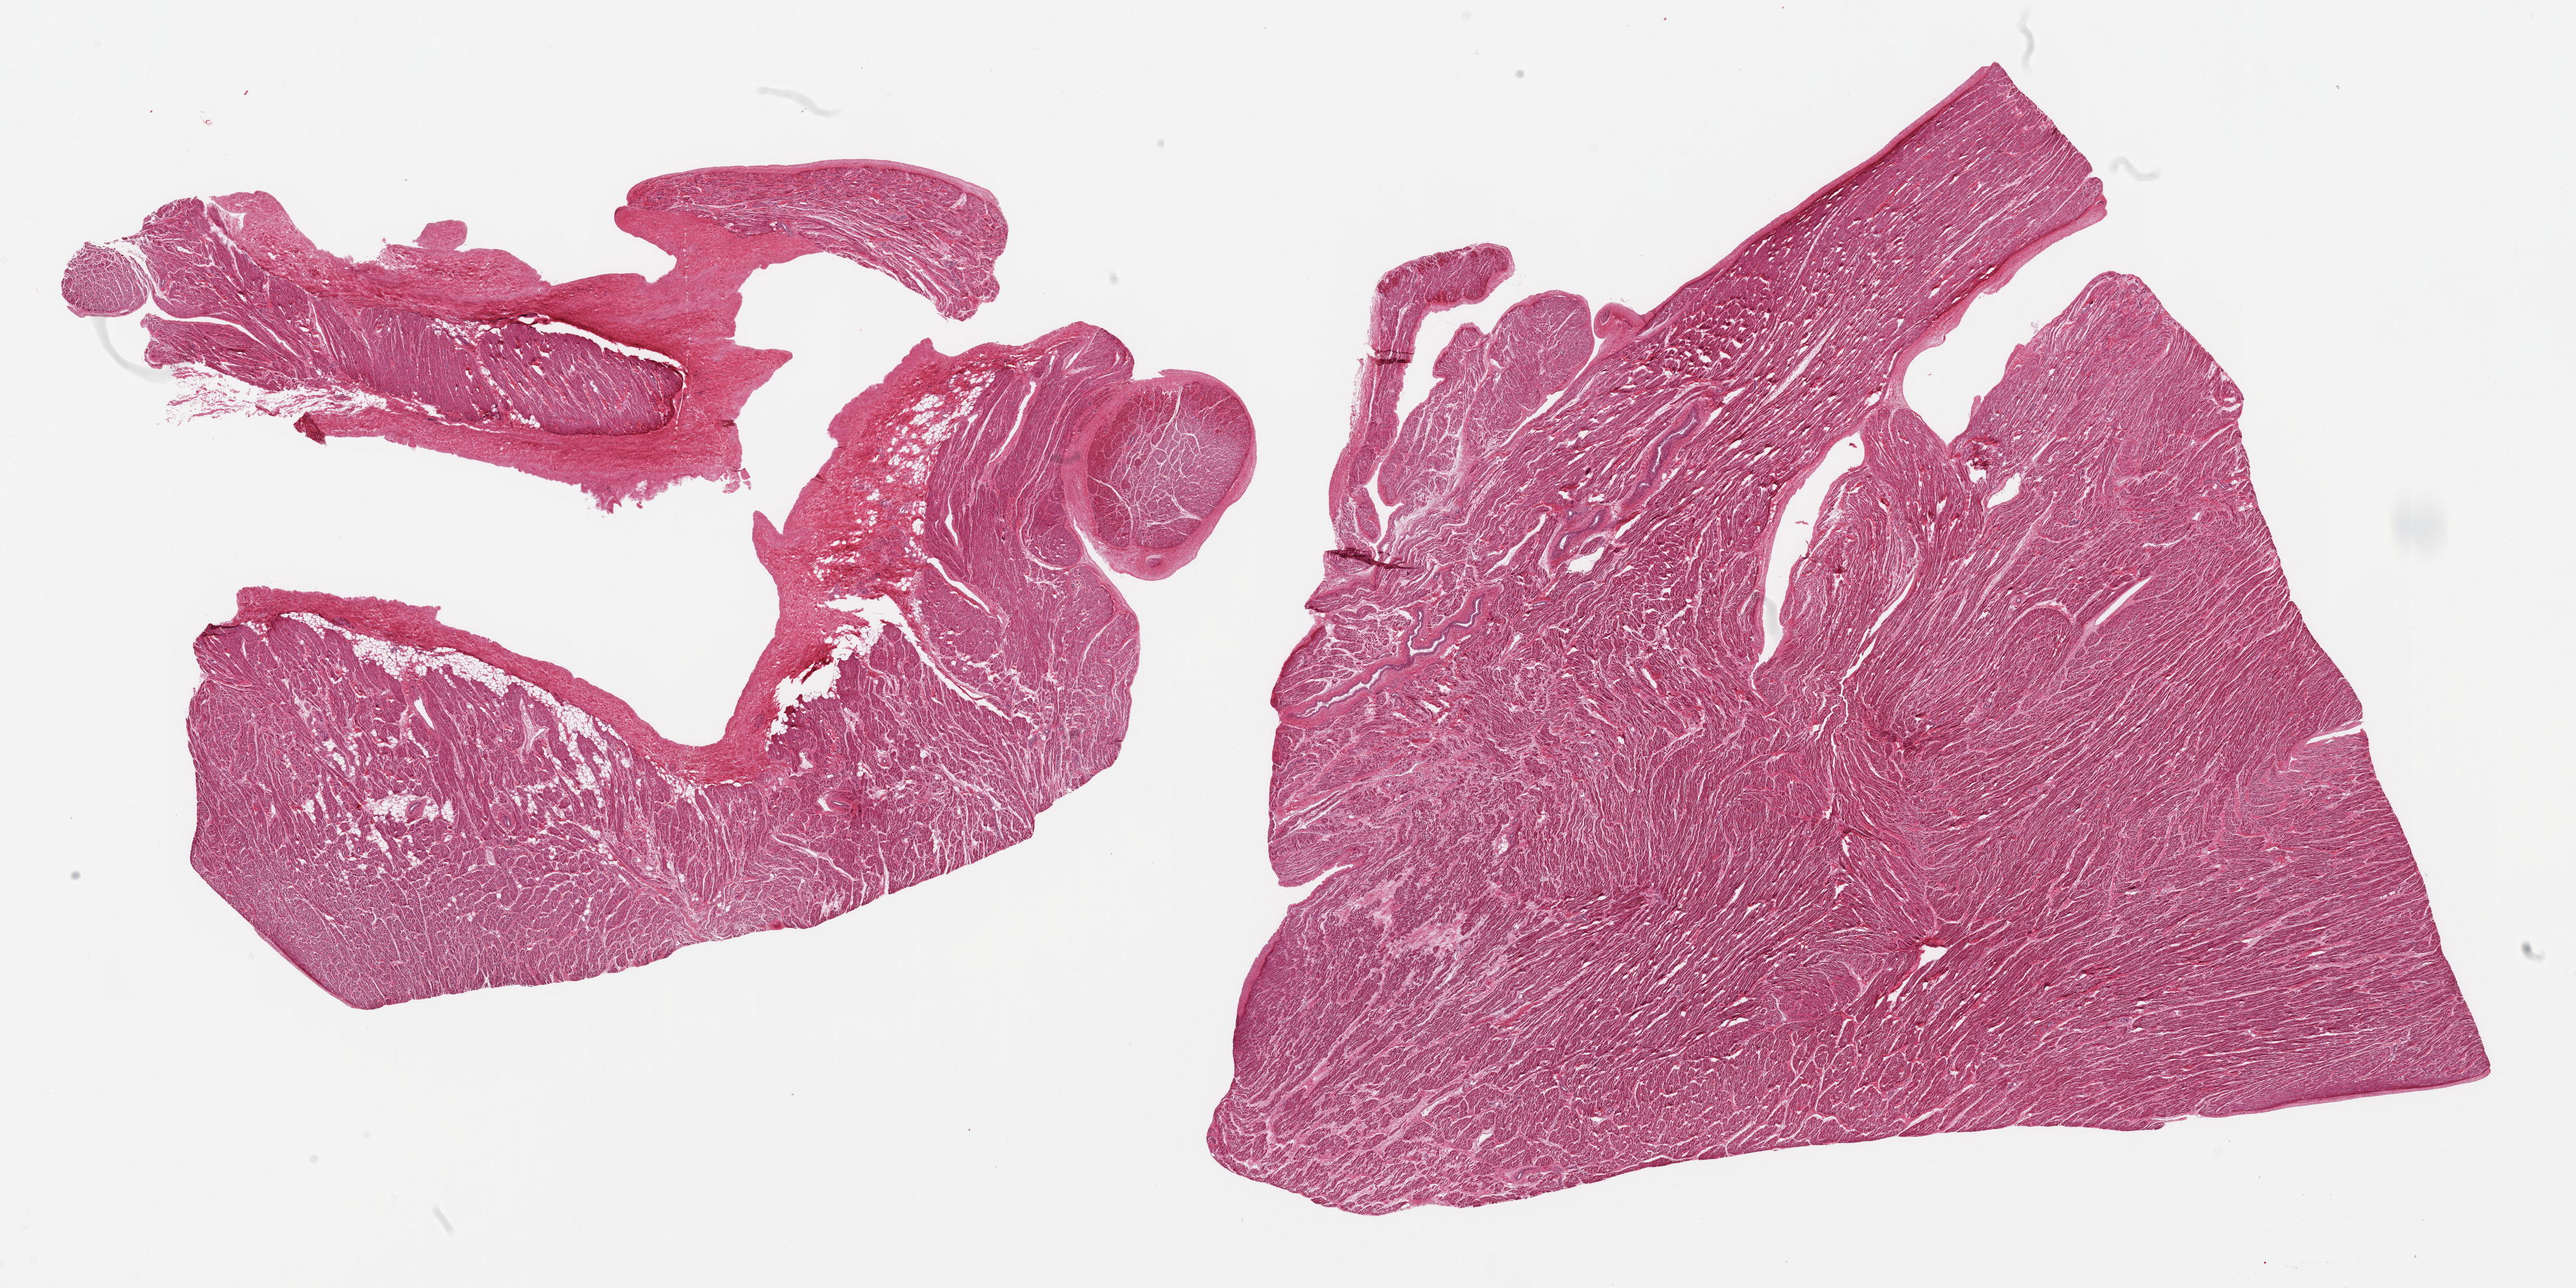
Digitized haematoxylin and eosin-stained section — whole scanned area (about 30.5 x 15.3 mm) shown as a low-resolution overview, PAXgene-fixed paraffin-embedded (PFPE) section, target tissue: auricular appendage, tissue donor sample. Male donor.
Pathologist's review note for this sample: 2 pieces: smaller has 20% fibrofatty content.